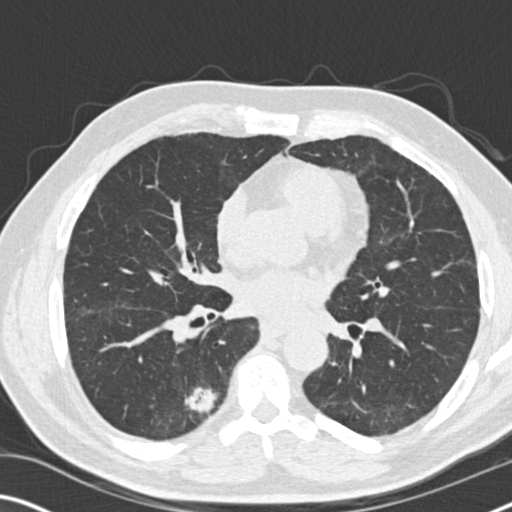
Low-dose screening chest CT, one axial slice. Slice 83 of 169 in the series (ordered by position). Reconstruction kernel B30f. 120 kVp. Lung window (W 1500 / L -600 HU). 2 mm slice thickness. 512 × 512 image matrix.
Annotated regions visible in this slice (outlined manually by an expert reader):
- lesion 1 (tumor, lower lobe of right lung): bounding box (x1, y1, x2, y2) in pixels: (185, 387, 216, 414)